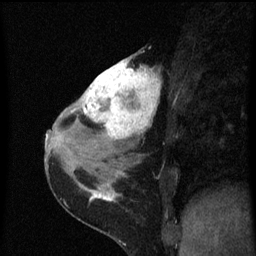
Breast MRI (dynamic contrast-enhanced), one sagittal slice; position 30 of 60 along the scan axis; dynamic contrast-enhanced series, image 2 of 3 at this slice position (ordered by acquisition); 1.5 T; TE 4.2 ms, TR 8 ms; 2 mm slice thickness; 256 × 256 image matrix, field of view 180 × 180 mm. Patient: female, 38 years.
Outlined on this slice (semi-automatically segmented with operator editing):
- analysis volume of interest (the breast-tissue region the enhancement analysis was run in; not a lesion): bounding box (x1, y1, x2, y2) in pixels: (80, 52, 163, 151)
- tumour enhancement mask (voxels above the 70 % enhancement threshold inside the analysis volume of interest): (80, 58, 161, 141)